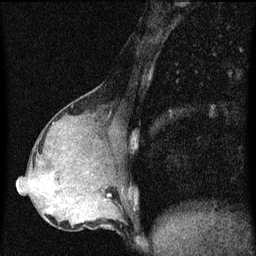
Breast MRI (dynamic contrast-enhanced), one sagittal slice. Position 27 of 60 along the scan axis. Dynamic contrast-enhanced series, image 2 of 3 at this slice position (ordered by acquisition). 1.5 T. TE 4.2 ms, TR 8 ms. 2 mm slice thickness. 256 × 256 image matrix, field of view 180 × 180 mm. Patient: female, 49 years.
Annotated regions visible in this slice (semi-automatically segmented with operator editing):
- analysis volume of interest (the breast-tissue region the enhancement analysis was run in; not a lesion): box from (x=43, y=190) to (x=88, y=219) px
- tumour enhancement mask (voxels above the 70 % enhancement threshold inside the analysis volume of interest): (x=49, y=208)–(x=52, y=213)